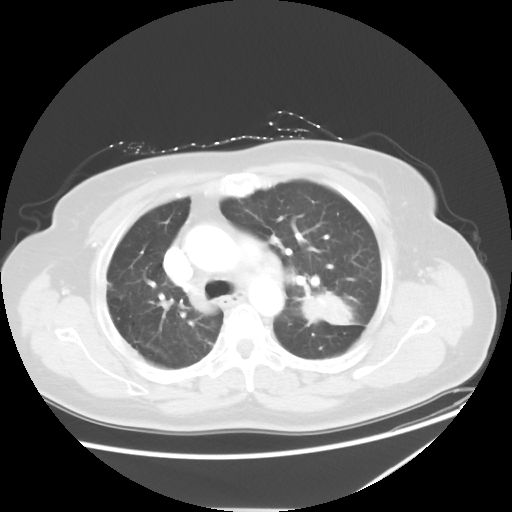
Chest CT, one axial slice; position 38 of 54 along the scan axis; reconstruction kernel STANDARD; 120 kVp; lung window (W 1500 / L -600 HU); 5 mm slice thickness; 512 × 512 image matrix, field of view 384 × 384 mm. Female patient, age 61 years. From the clinical record (not read from this slice): clinical TNM (as recorded): T1c N3 M1.
Structures marked on this image (rectangle marked by the reading radiologist):
- lung tumour (recorded histology: adenocarcinoma): bounding box (x1, y1, x2, y2) in pixels: (301, 287, 359, 332)